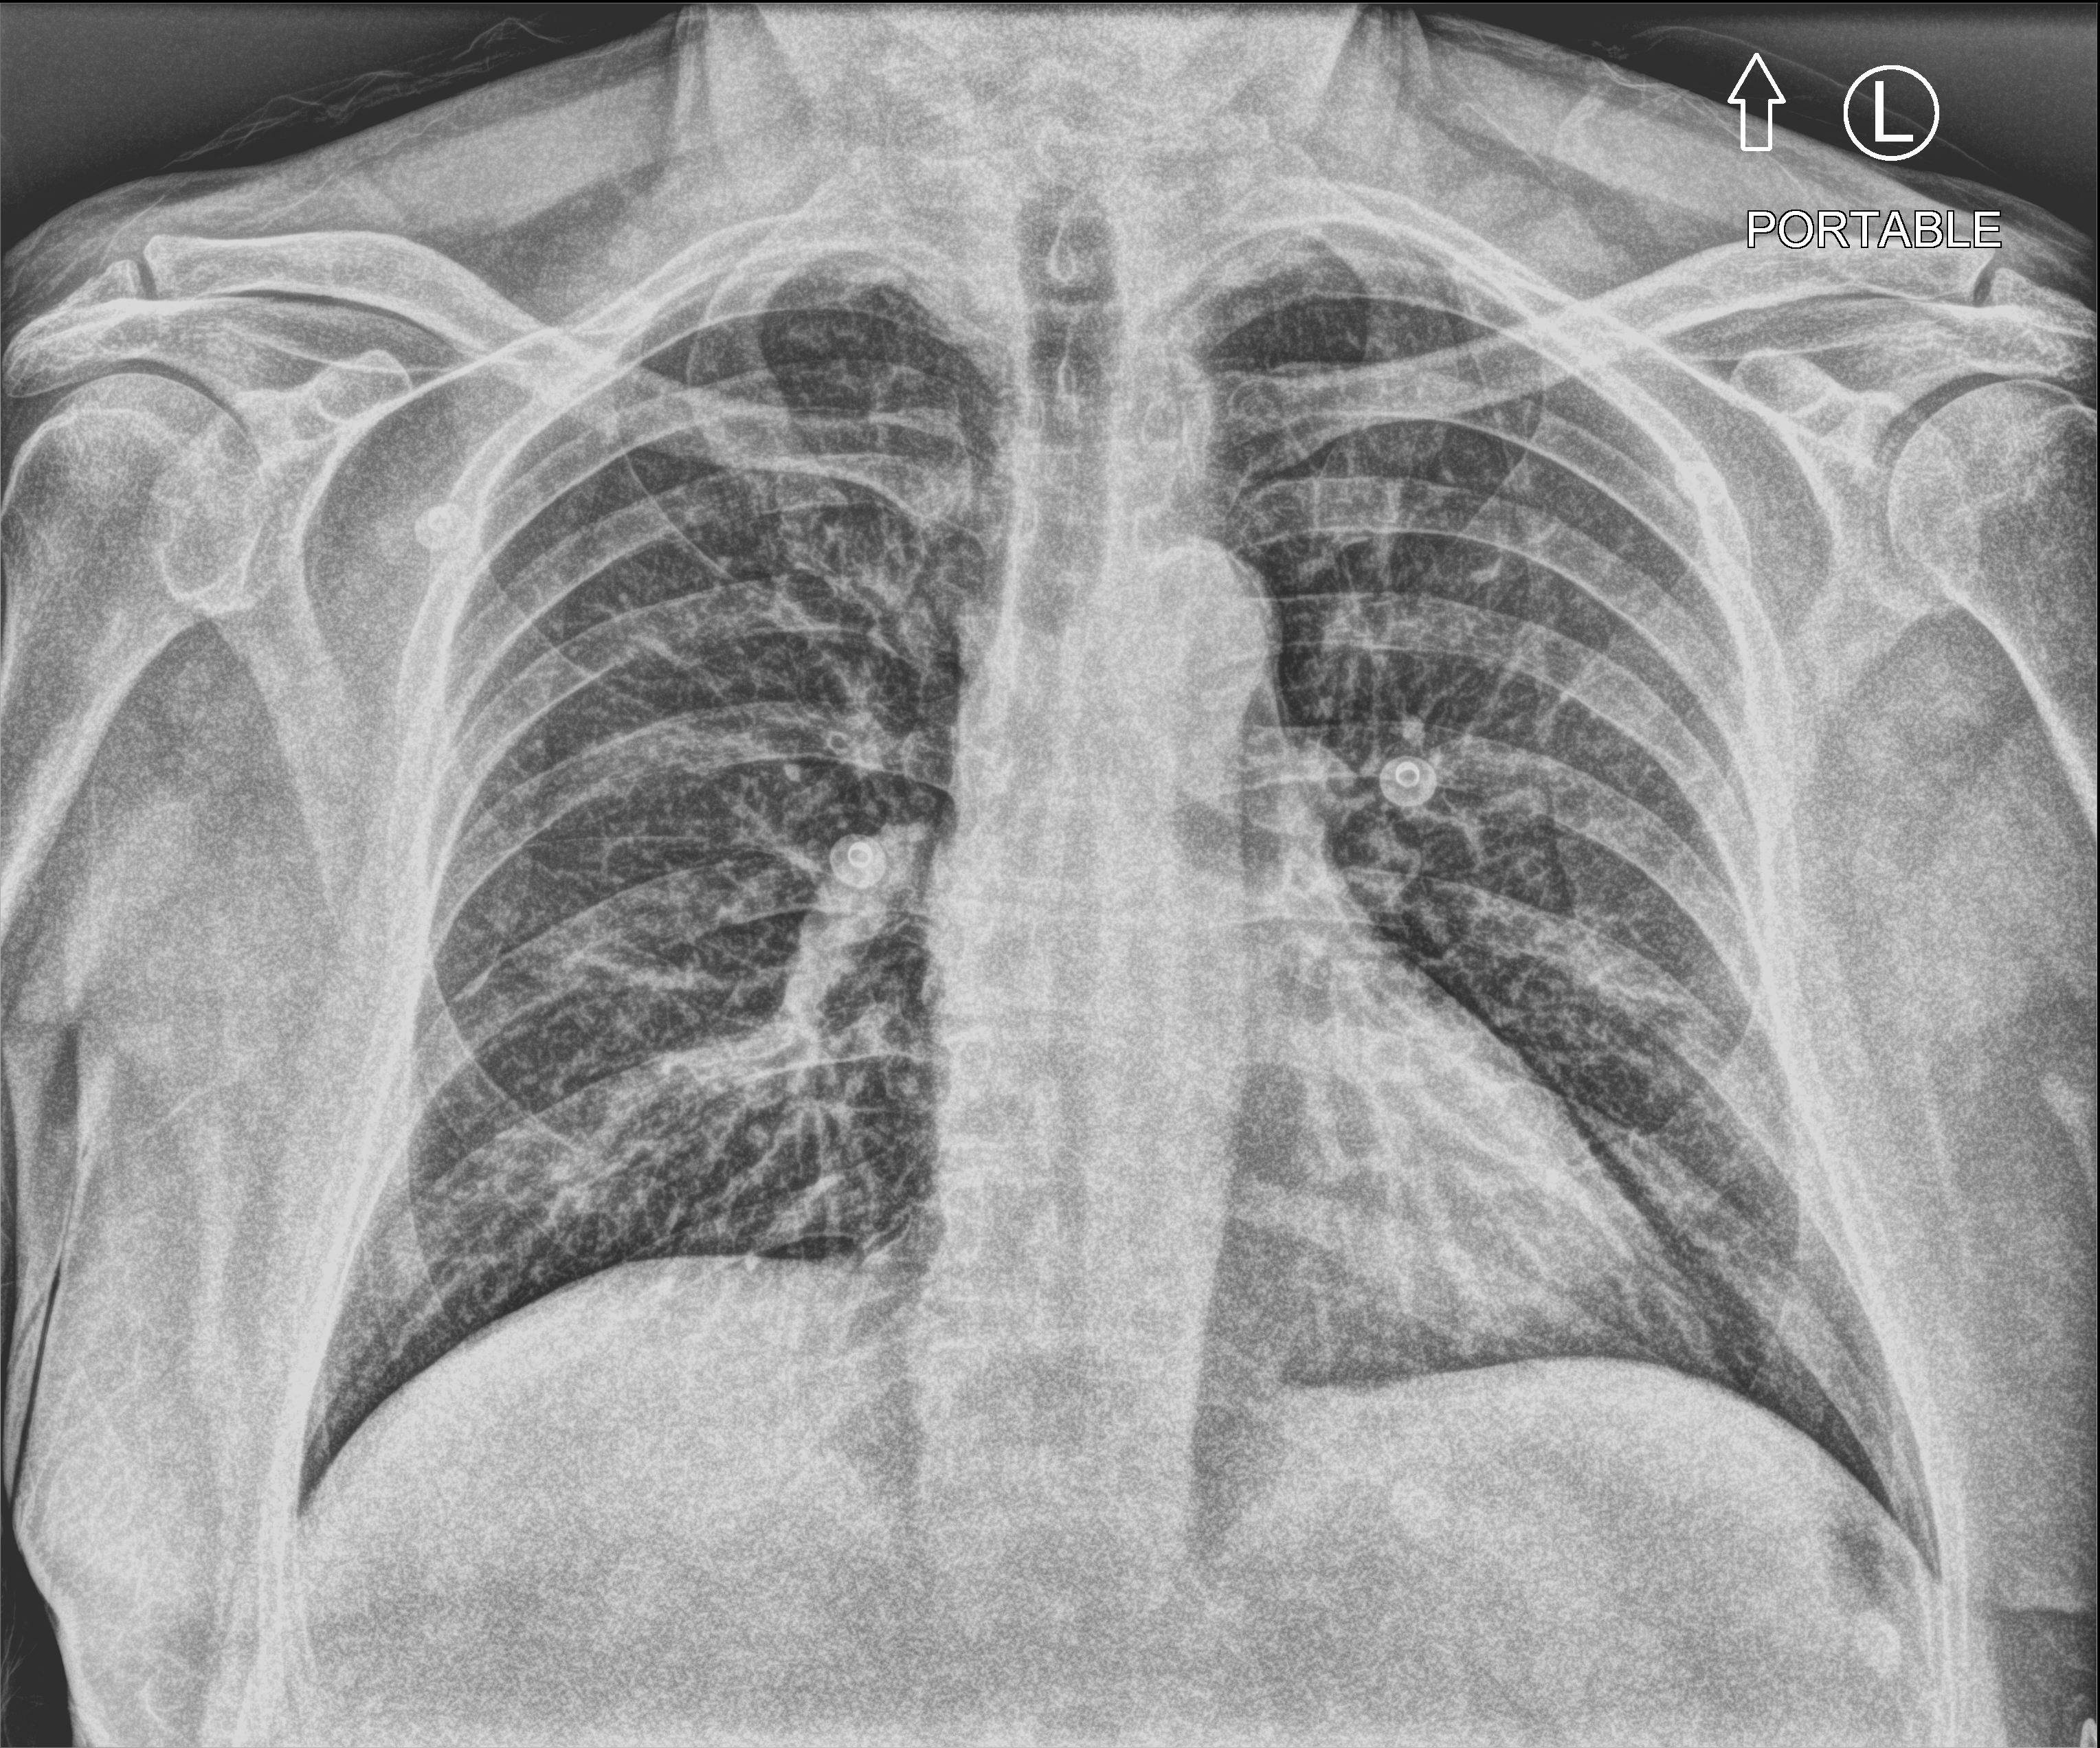
Bedside chest radiograph (computed radiography), anteroposterior (AP) projection. Male patient hospitalised with COVID-19, age 60–74 years.
From the hospital-stay record, not from the radiograph (when in the stay this image was taken is not recorded): mechanically ventilated during this hospital stay: no; length of hospital stay: 1 day.